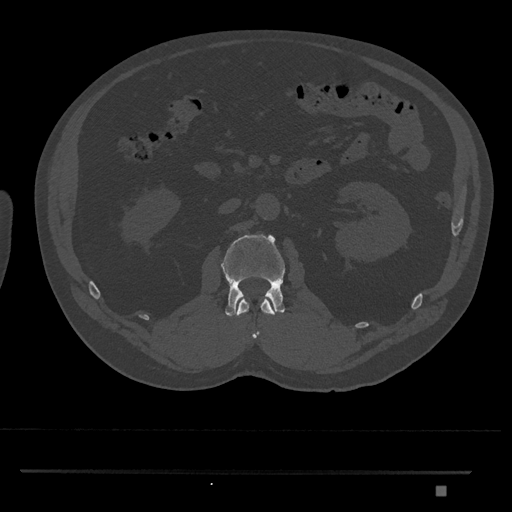
CT including the spine, one axial slice; reconstruction kernel Br40s/3; bone window (W 1800 / L 400 HU); 512 × 512 image matrix, field of view 429 × 429 mm. Patient: male, 65 years. Case-level facts recorded for this patient, not image findings: primary cancer: prostate.
Structures marked on this image (semi-automatically segmented with operator editing):
- L1 vertebra: box from (x=236, y=298) to (x=275, y=339) px
- L2 vertebra: (x=221, y=234)–(x=286, y=316)